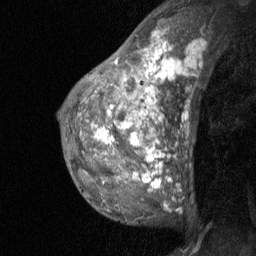
Breast MRI (dynamic contrast-enhanced), one sagittal slice; slice 41 of 64 in the series (ordered by position); dynamic contrast-enhanced study with each time point stored as its own series, time point 2 of 3 at this slice position (early post-contrast, ordered by acquisition time); 1.5 T; TE 4.8 ms, TR 27 ms; 2 mm slice thickness; 256 × 256 image matrix. Patient: female, 36 years. From the clinical record (not read from this slice): setting: breast cancer imaged before/during neoadjuvant chemotherapy; receptor status: HR-positive, HER2-negative.
Structures marked on this image (semi-automatically segmented with operator editing):
- analysis volume of interest (the breast-tissue region the enhancement analysis was run in; not a lesion): bounding box [x1, y1, x2, y2] px = [67, 12, 194, 225]
- tumour enhancement mask (voxels above the 90 % enhancement threshold inside the analysis volume of interest): [92, 32, 164, 191]